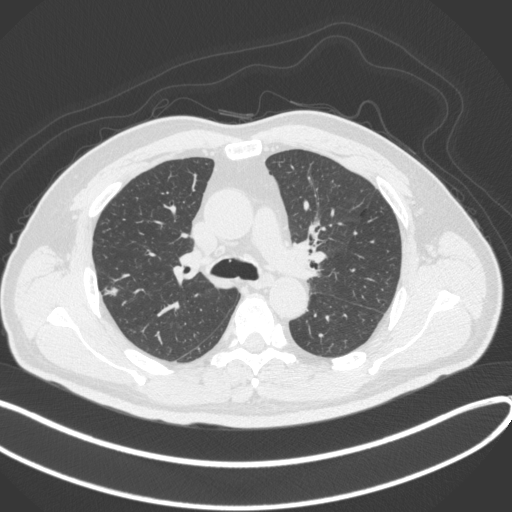
Chest CT, one axial slice. Slice 225 of 373 in the series (ordered by position). Lung window (W 1500 / L -600 HU). 1 mm slice thickness. 512 × 512 image matrix, field of view 400 × 400 mm. Patient: male, 60 years. Case-level facts recorded for this patient, not image findings: clinical TNM (as recorded): T1c N0 M0.
Outlined on this slice (bounding box drawn by a radiologist):
- lung tumour (recorded histology: adenocarcinoma): bounding box <98,281,121,301> (left, top, right, bottom; pixels)